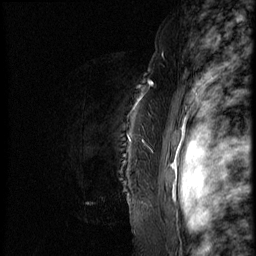
Breast MRI (dynamic contrast-enhanced), one sagittal slice; position 61 of 66 along the scan axis; dynamic contrast-enhanced series, image 2 of 3 at this slice position (ordered by acquisition); 1.5 T; TE 4.2 ms, TR 8.9 ms; 2.5 mm slice thickness; 256 × 256 image matrix, field of view 200 × 200 mm. Female patient, age 39 years. From the clinical record (not read from this slice): setting: breast cancer imaged before/during neoadjuvant chemotherapy; receptor status: HER2-positive.
Structures marked on this image (semi-automatically segmented with operator editing):
- analysis volume of interest (the breast-tissue region the enhancement analysis was run in; not a lesion): bounding box (x1, y1, x2, y2) in pixels: (71, 75, 159, 218)
- tumour enhancement mask (voxels above the 140 % enhancement threshold inside the analysis volume of interest): (150, 82, 153, 85)